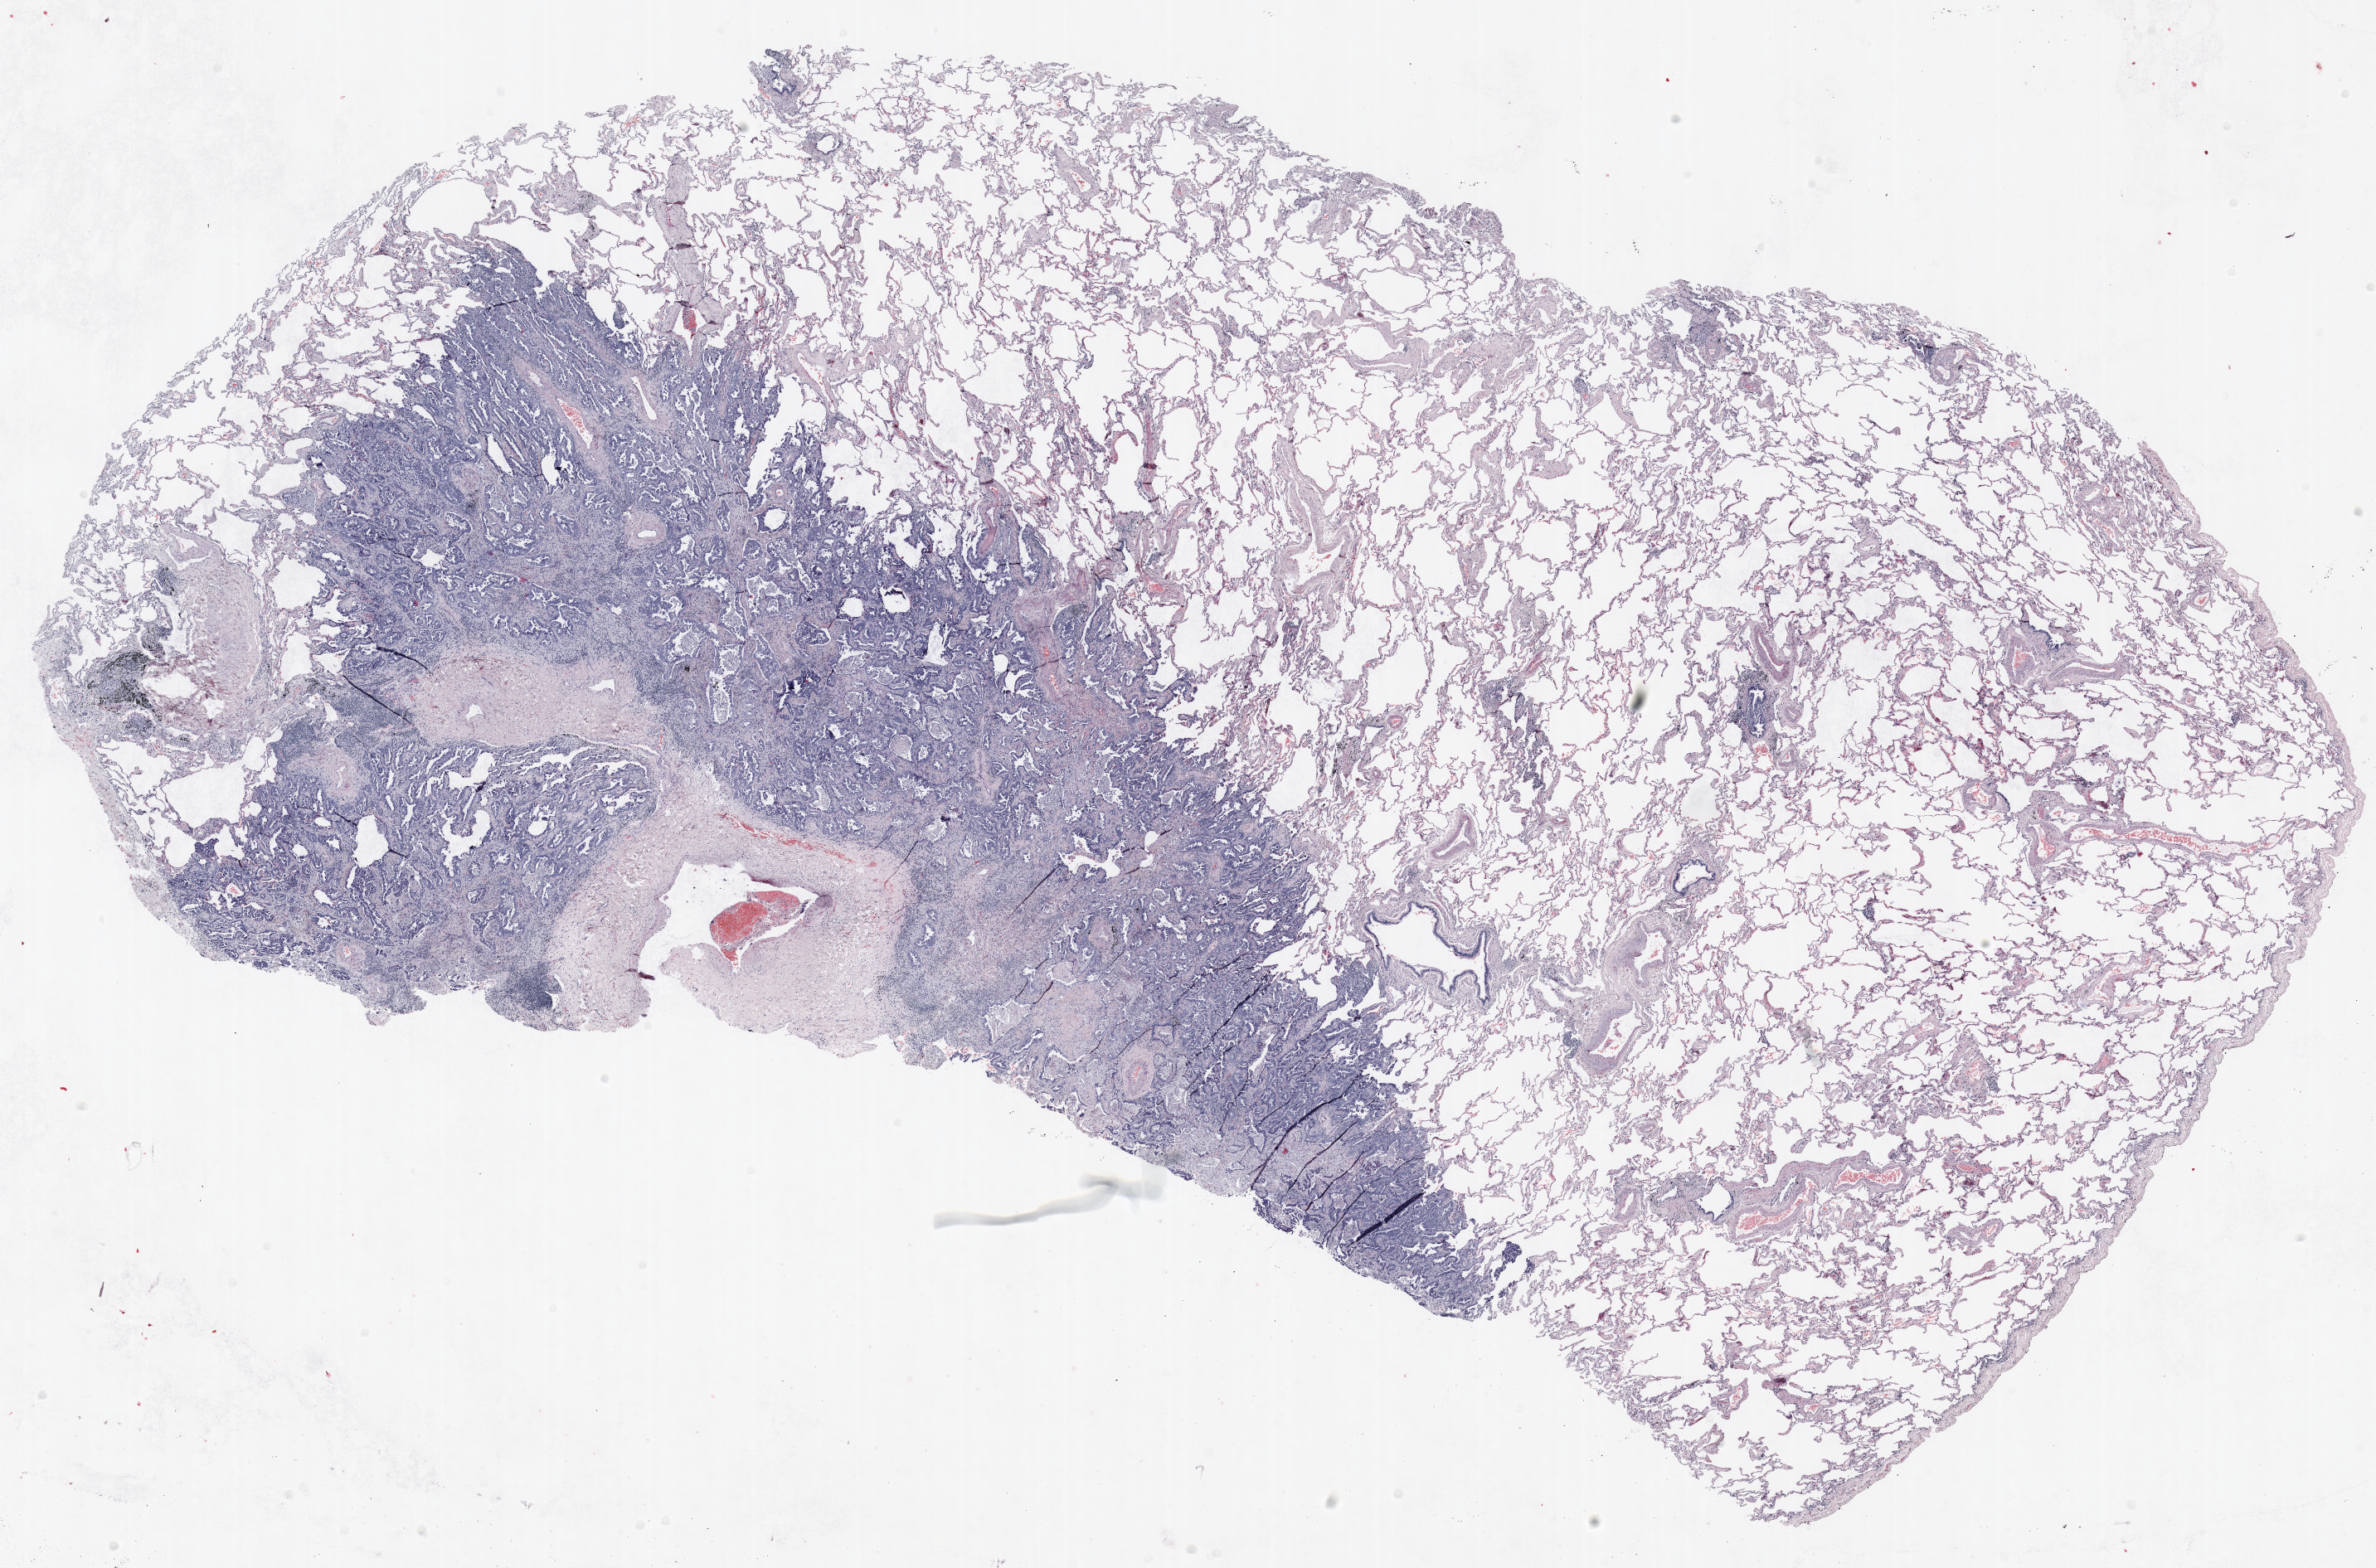
Hematoxylin and eosin (H&E) stained whole-slide image — low-resolution overview of the scanned area, about 23.0 x 15.2 mm. Formalin-fixed paraffin-embedded (FFPE) section. Lung. Female, age 68 at enrolment. Former smoker at enrolment. Grade: moderately differentiated (G2).
Primary tumour location (clinical record): right upper lobe. Participant's lung-cancer diagnosis: Adenocarcinoma, NOS (ICD-O-3 8140/3). Stage (AJCC 6th edition): IB. Tumour size (pathology): 31 mm.